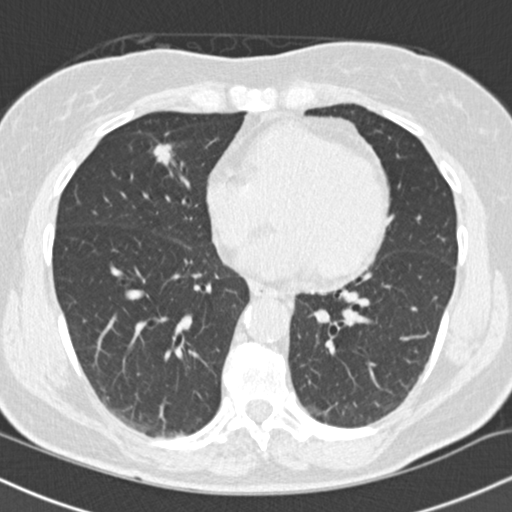
Chest CT (low-dose screening protocol), one axial image. First (baseline) screen. Lung window (W 1500 / L -600 HU). Female, age 66 years at enrolment. Current smoker at enrolment.
Expert-annotated lung lesion, bounding box <139,135,181,171> (left, top, right, bottom; pixels). Screening reader's record for this exam (one nodule recorded; not confirmed to be the boxed lesion): non-calcified nodule or mass ≥4 mm, right lower lobe, 10 × 8 mm, smooth margins, soft tissue attenuation. Official screen result: positive, change unspecified: nodule(s) >= 4 mm or enlarging nodule(s), mass(es), or other non-specific abnormalities suspicious for lung cancer.